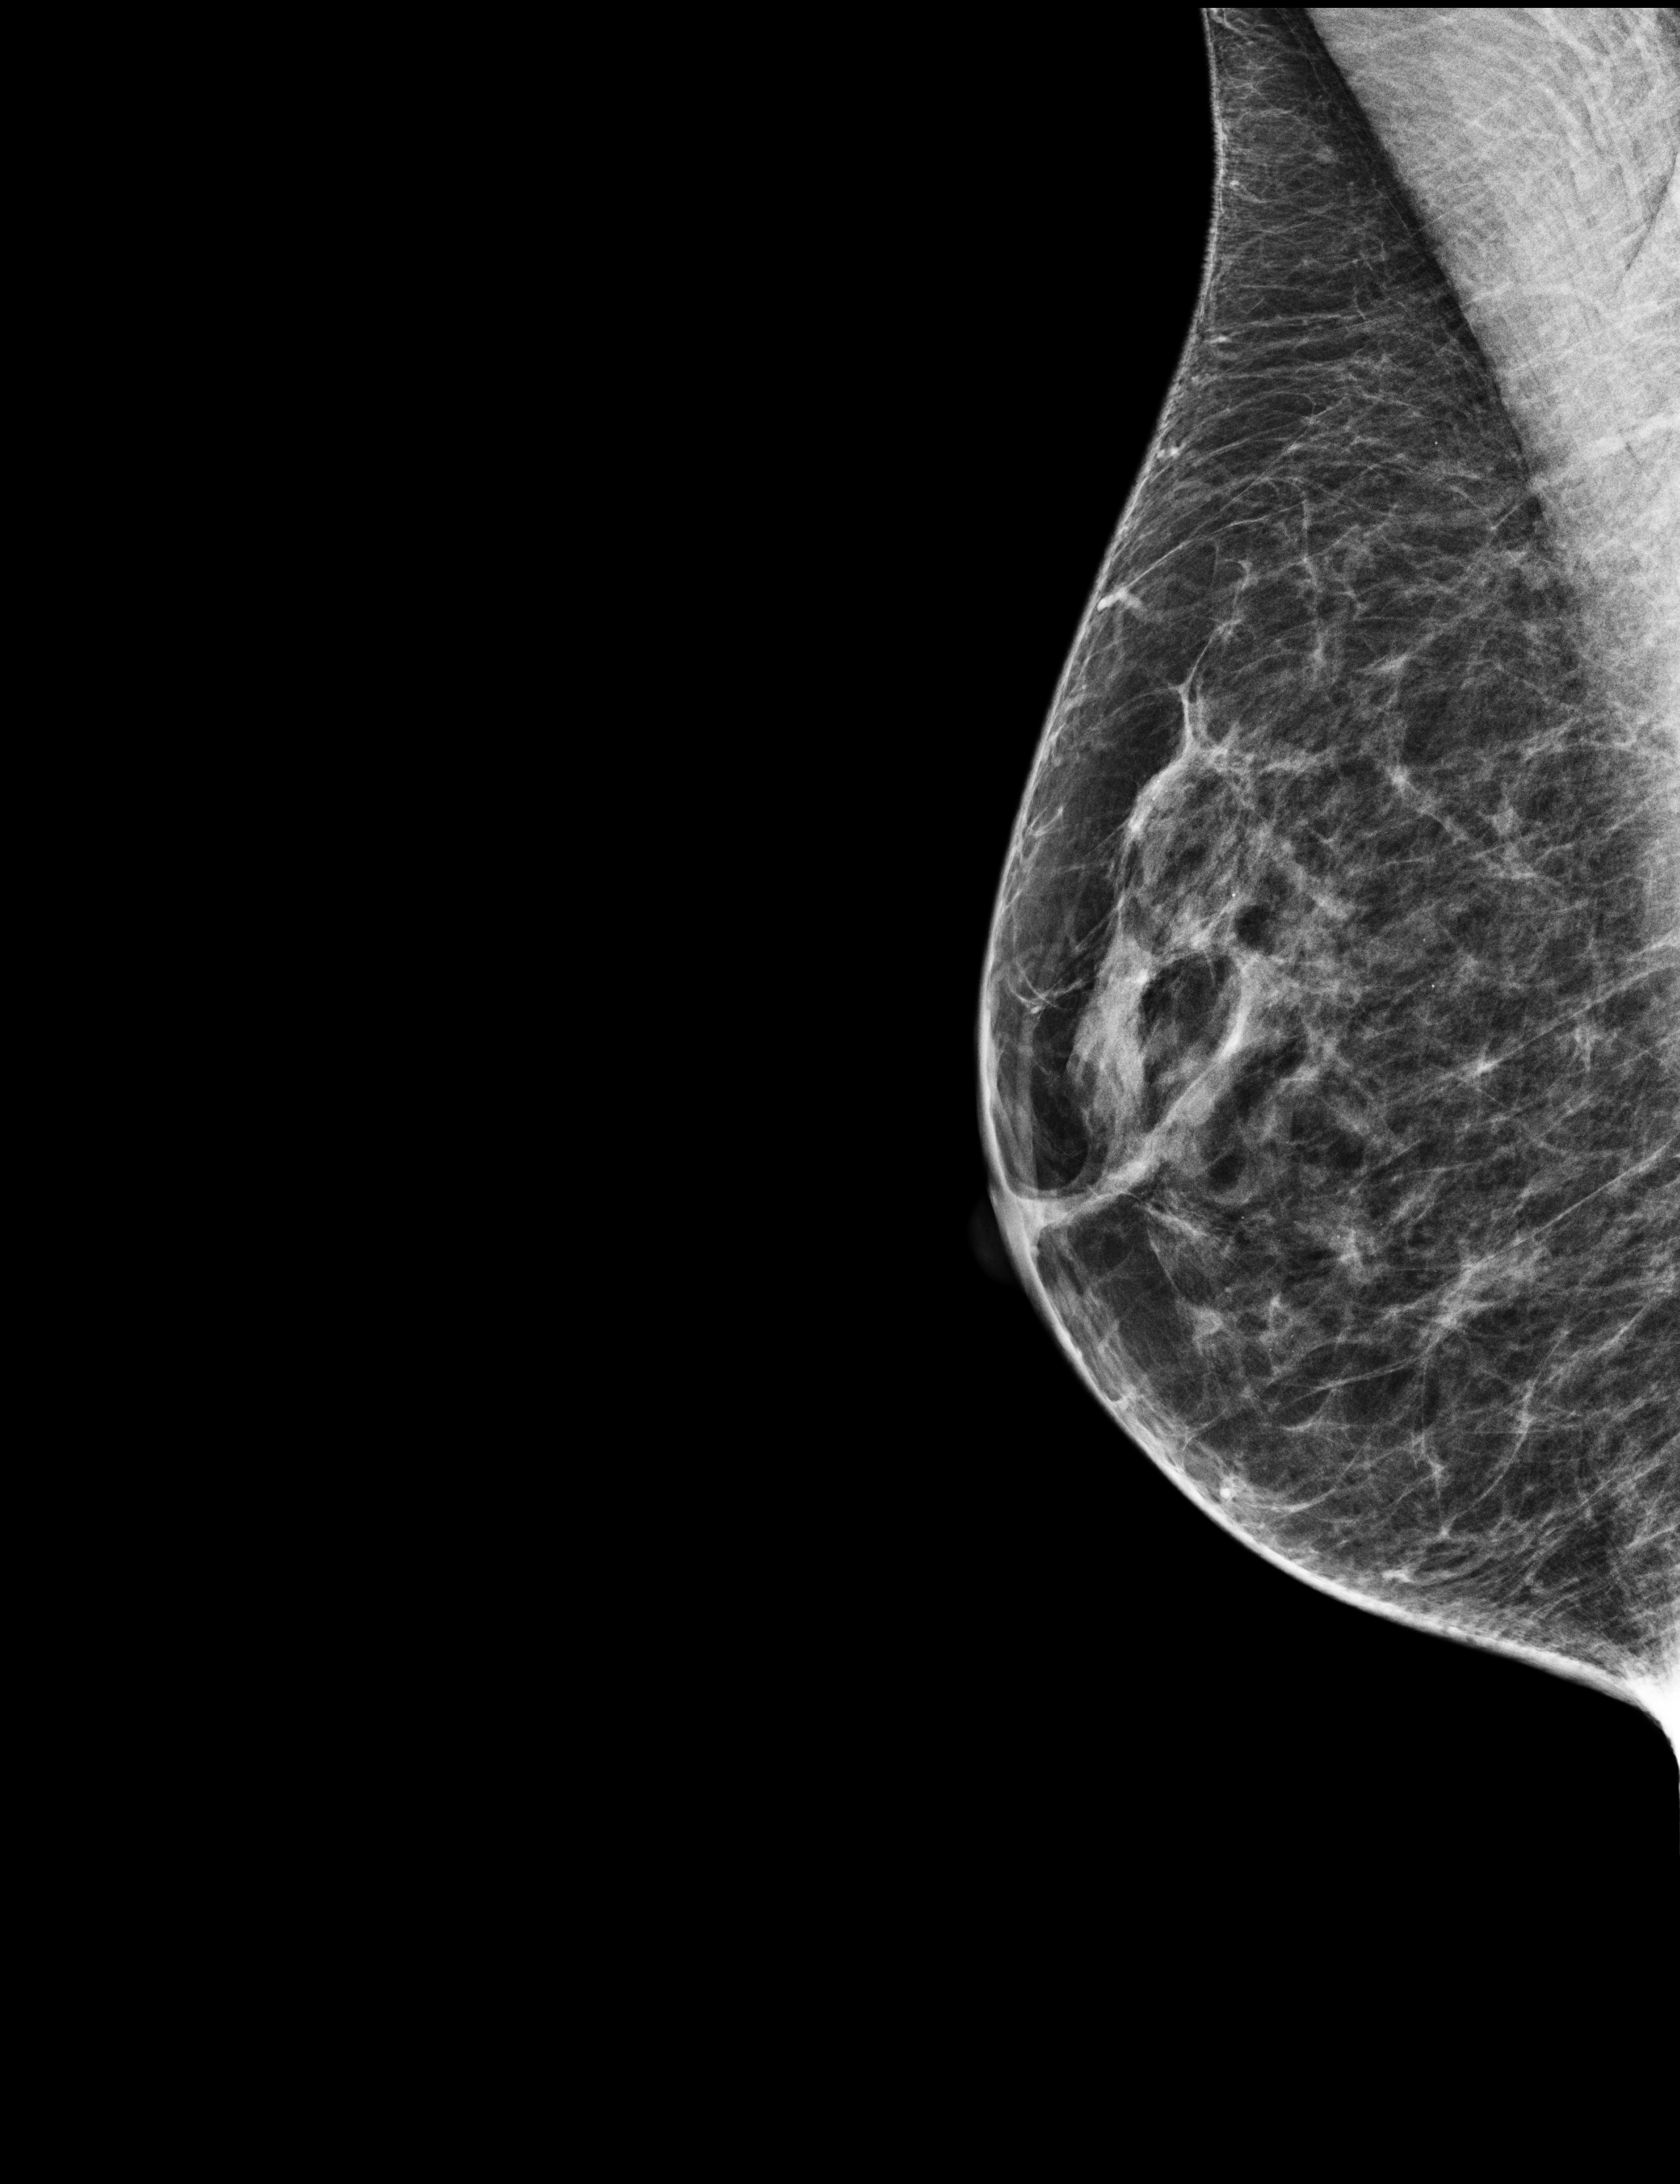
Full-field digital mammogram (FFDM), right breast, mediolateral oblique (MLO) view, annual screening mammography examination, compressed breast thickness 47 mm. Patient: female, 67 years.
Final BI-RADS assessment for this screening round (tomosynthesis exam, both breasts): category 2.